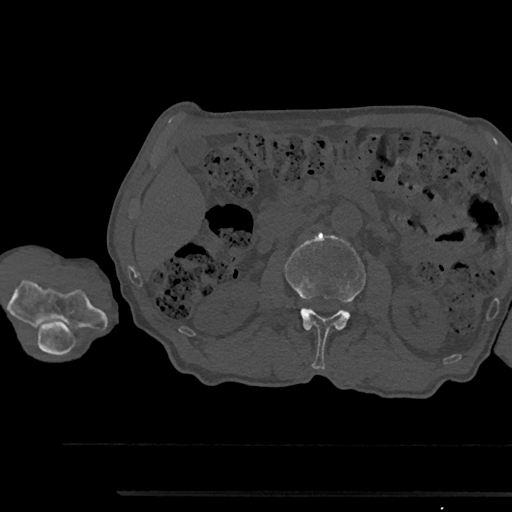
CT including the spine, one axial slice. Position 557 of 797 along the scan axis. 120 kVp. Bone window (W 1800 / L 400 HU). 0.5 mm slice thickness. 512 × 512 image matrix, field of view 367 × 367 mm. Patient: male, 79 years. From the clinical record (not read from this slice): primary cancer: prostate.
Outlined on this slice (semi-automatically segmented with operator editing):
- L2 vertebra: box from (x=285, y=233) to (x=366, y=369) px